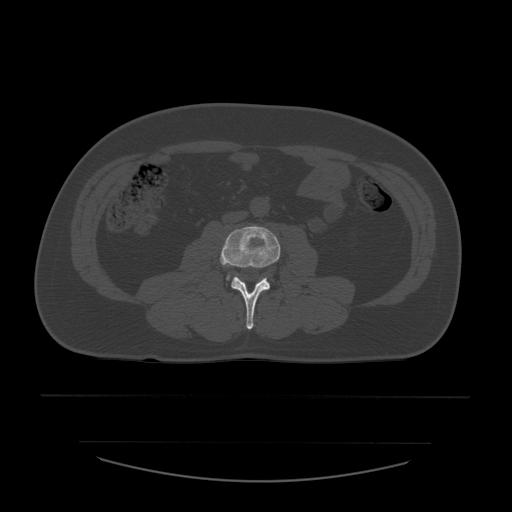
CT including the spine, one axial slice; slice 166 of 532 in the series (ordered by position); reconstruction kernel STANDARD; 120 kVp; bone window (W 1800 / L 400 HU); 1.25 mm slice thickness; 512 × 512 image matrix. Patient age 44 years. From the clinical record (not read from this slice): primary cancer: soft tissue sarcoma.
Annotated regions visible in this slice (semi-automatically segmented with operator editing):
- L3 vertebra: bounding box <220,226,281,330> (left, top, right, bottom; pixels)
- L4 vertebra: <227,276,234,280>